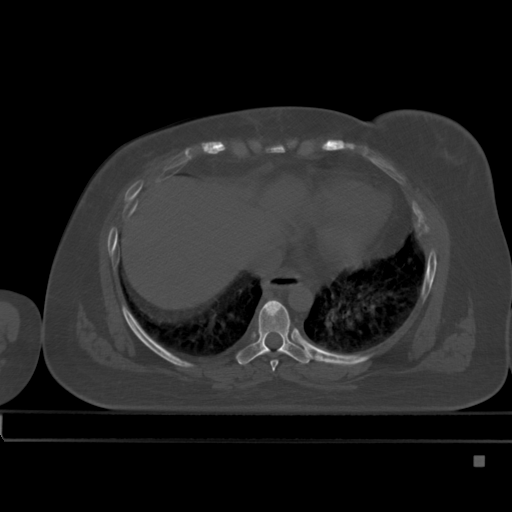
CT including the spine, one axial slice. Slice 280 of 495 in the series (ordered by position). Bone window (W 1800 / L 400 HU). 1.5 mm slice thickness. 512 × 512 image matrix, field of view 404 × 404 mm. Female patient, age 33 years. Case-level facts recorded for this patient, not image findings: primary cancer: breast.
Outlined on this slice (semi-automatic segmentation, software-assisted and operator-edited):
- T7 vertebra: bounding box <271,360,278,371> (left, top, right, bottom; pixels)
- T8 vertebra: <236,300,311,365>